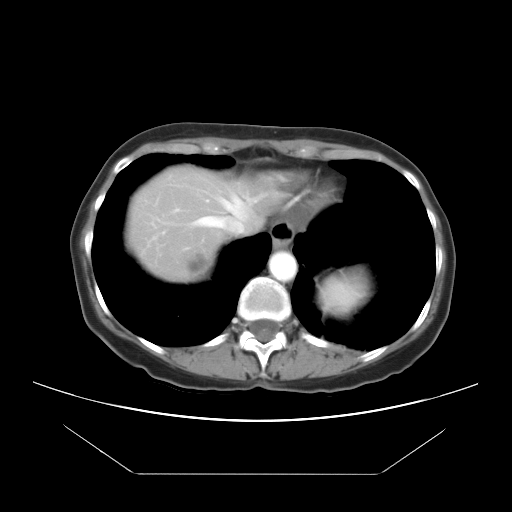
Contrast-enhanced abdominal CT, one axial slice; position 19 of 21 along the scan axis; reconstruction kernel STANDARD; intravenous contrast given; soft-tissue window (W 400 / L 40 HU); 7.5 mm slice thickness; 512 × 512 image matrix. Female patient, age 72 years. Case-level facts recorded for this patient, not image findings: diagnosis: colorectal cancer liver metastases, imaged before liver resection; multiple liver metastases: yes; largest metastasis: 4 cm; disease in both lobes: yes.
Structures marked on this image (expert manual segmentation):
- hepatic veins: bounding box [x1, y1, x2, y2] px = [197, 197, 245, 227]
- liver: [128, 167, 275, 279]
- planned liver remnant (the part of the liver to remain after resection): [128, 167, 275, 254]
- liver metastasis: [185, 252, 210, 276]